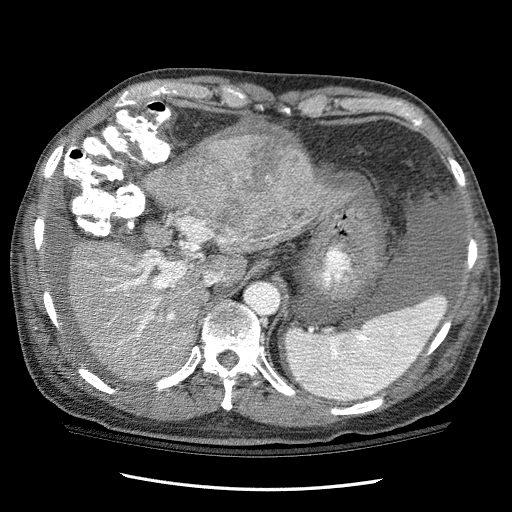
Contrast-enhanced abdominal CT (liver protocol), one axial slice. Slice 78 of 114 in the series (ordered by position). Reconstruction kernel STANDARD. 120 kVp. One of 3 acquisitions stored at this slice position. Soft-tissue window (W 400 / L 40 HU). 2.5 mm slice thickness. 512 × 512 image matrix, field of view 360 × 360 mm. From the clinical record (not read from this slice): diagnosis: hepatocellular carcinoma (patient treated with transarterial chemoembolisation; whether this scan precedes or follows treatment is not stated here); TNM stage (as recorded): Stage-I; Child-Pugh class: C; tumour differentiation: well differentiated.
Outlined on this slice (semi-automatically segmented with operator editing):
- liver parenchyma outside the tumour (the mass and vessels are separate outlines, so this box may not span the whole liver): bounding box <58,149,338,388> (left, top, right, bottom; pixels)
- mass: <203,118,315,239>
- liver vessels: <106,229,274,344>